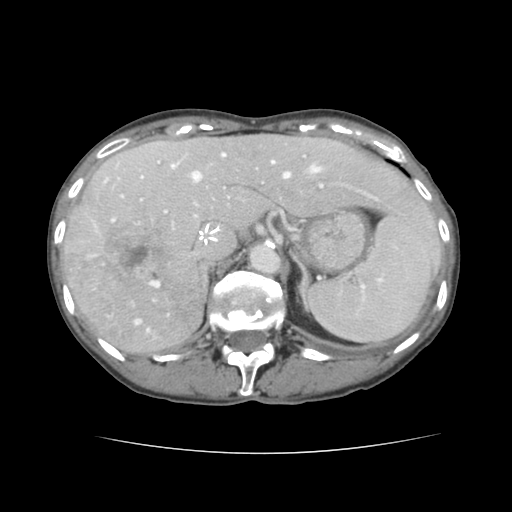
Contrast-enhanced abdominal CT, one axial slice; slice 100 of 136 in the series (ordered by position); 120 kVp; intravenous contrast given; soft-tissue window (W 400 / L 40 HU); 2.5 mm slice thickness; 512 × 512 image matrix, field of view 319 × 319 mm. Female patient, age 77 years. Case-level facts recorded for this patient, not image findings: diagnosis: colorectal cancer liver metastases, imaged before liver resection; multiple liver metastases: yes; largest metastasis: 3 cm.
Structures marked on this image (expert manual segmentation):
- hepatic veins: bounding box (x1, y1, x2, y2) in pixels: (105, 153, 320, 332)
- liver: (65, 134, 441, 355)
- planned liver remnant (the part of the liver to remain after resection): (157, 134, 440, 258)
- portal vein (with intrahepatic branches): (111, 172, 380, 287)
- liver metastasis: (102, 223, 177, 296)